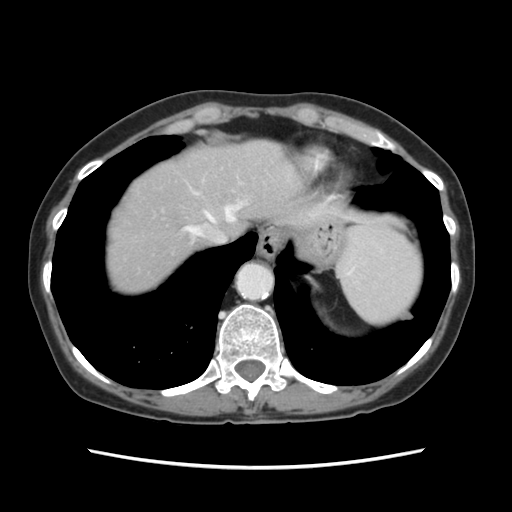
Contrast-enhanced abdominal CT, one axial slice. 120 kVp. Soft-tissue window (W 400 / L 40 HU). 512 × 512 image matrix. Female patient, age 70 years. From the clinical record (not read from this slice): diagnosis: colorectal cancer liver metastases, imaged before liver resection.
Outlined on this slice (manually delineated by an expert):
- hepatic veins: bounding box [x1, y1, x2, y2] px = [188, 205, 239, 243]
- liver: [107, 141, 301, 292]
- planned liver remnant (the part of the liver to remain after resection): [152, 141, 302, 251]